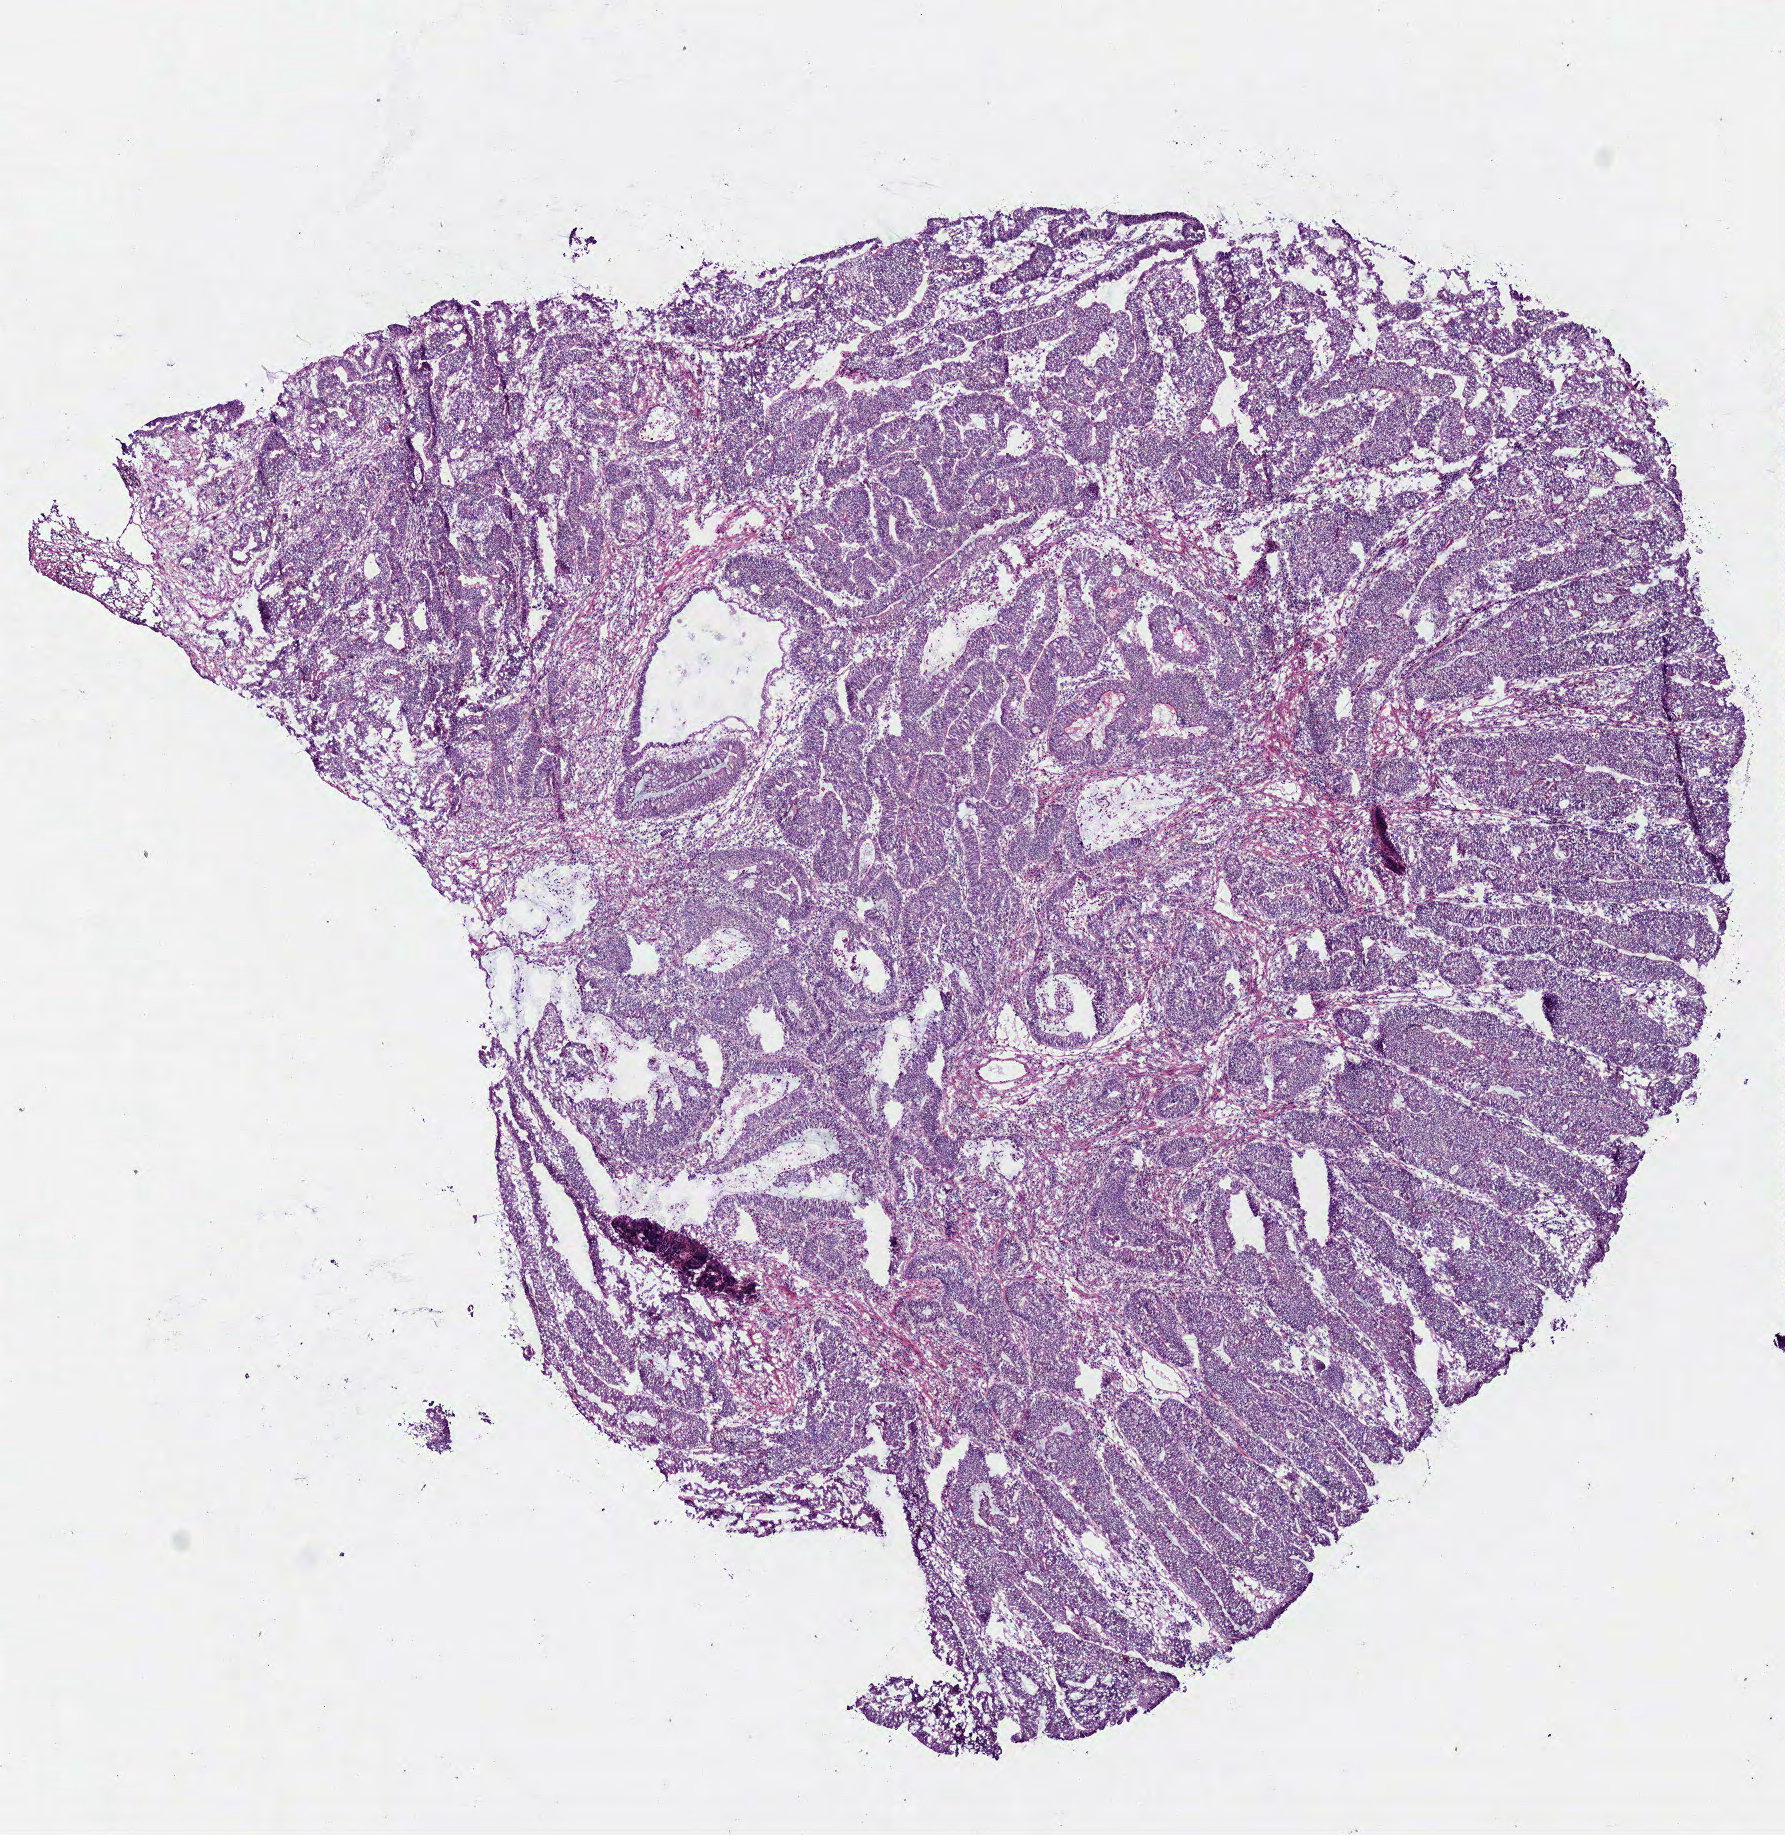
Digitized H&E tissue section (whole slide) — whole scanned area (about 7.0 x 7.2 mm, acquisition: 40x scan) shown as a low-resolution overview. Frozen section. Primary tumour sample from the colon. Female patient; age at initial diagnosis 46 years. Slide review estimates, as recorded: tumour cells 75%, tumour nuclei 80%, normal cells 15%, stromal cells 10%, necrosis 0%.
• lymph nodes positive (case pathology): 3 of 12 examined
• AJCC pathologic stage: IIIB (6th edition)
• histologic diagnosis: Adenocarcinoma, NOS (sigmoid colon)